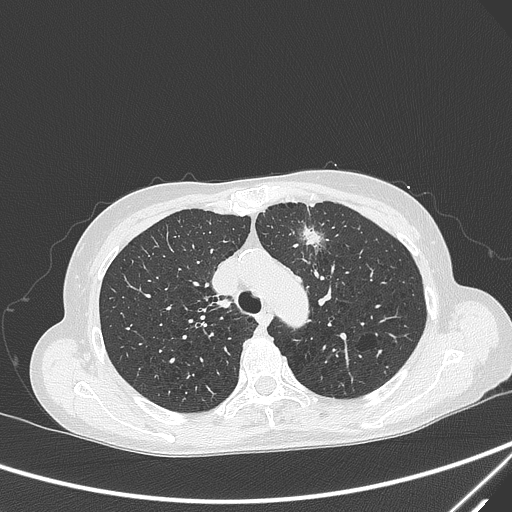
Chest CT, one axial slice; 120 kVp; lung window (W 1500 / L -600 HU); 512 × 512 image matrix. Female patient, age 71 years. From the clinical record (not read from this slice): clinical TNM (as recorded): T1c N0 M0; histopathological grade: G2-3.
Structures marked on this image (rectangle marked by the reading radiologist):
- lung tumour (recorded histology: adenocarcinoma): box from (x=298, y=219) to (x=328, y=257) px